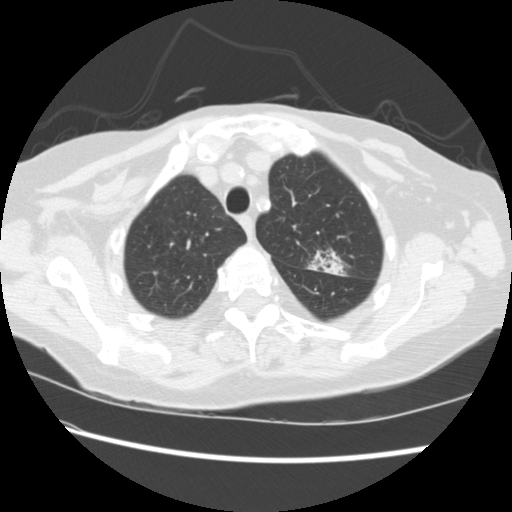
Low-dose screening chest CT, one axial slice. Position 179 of 224 along the scan axis. Reconstruction kernel STANDARD. Lung window (W 1500 / L -600 HU). 2.5 mm slice thickness. 512 × 512 image matrix, field of view 340 × 340 mm.
Annotated regions visible in this slice (manually delineated by an expert):
- lesion 1 (tumor, upper lobe of left lung): bounding box [x1, y1, x2, y2] px = [320, 259, 345, 276]